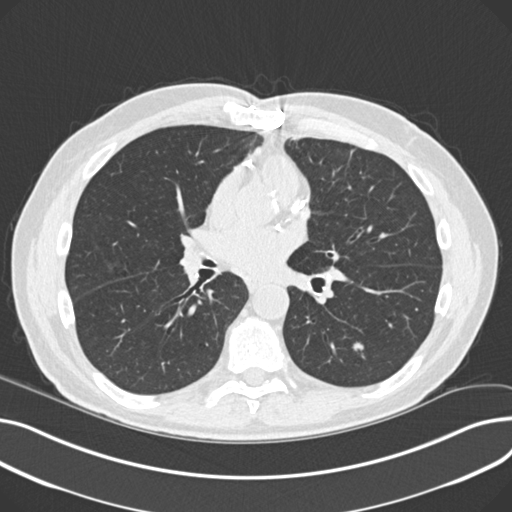
Low-dose screening chest CT, one axial slice. Position 110 of 230 along the scan axis. Reconstruction kernel B30f. Lung window (W 1500 / L -600 HU). 2 mm slice thickness. 512 × 512 image matrix, field of view 372 × 372 mm.
Structures marked on this image (expert manual segmentation):
- lesion 3 (nodule, lower lobe of left lung): bounding box (x1, y1, x2, y2) in pixels: (353, 342, 365, 351)